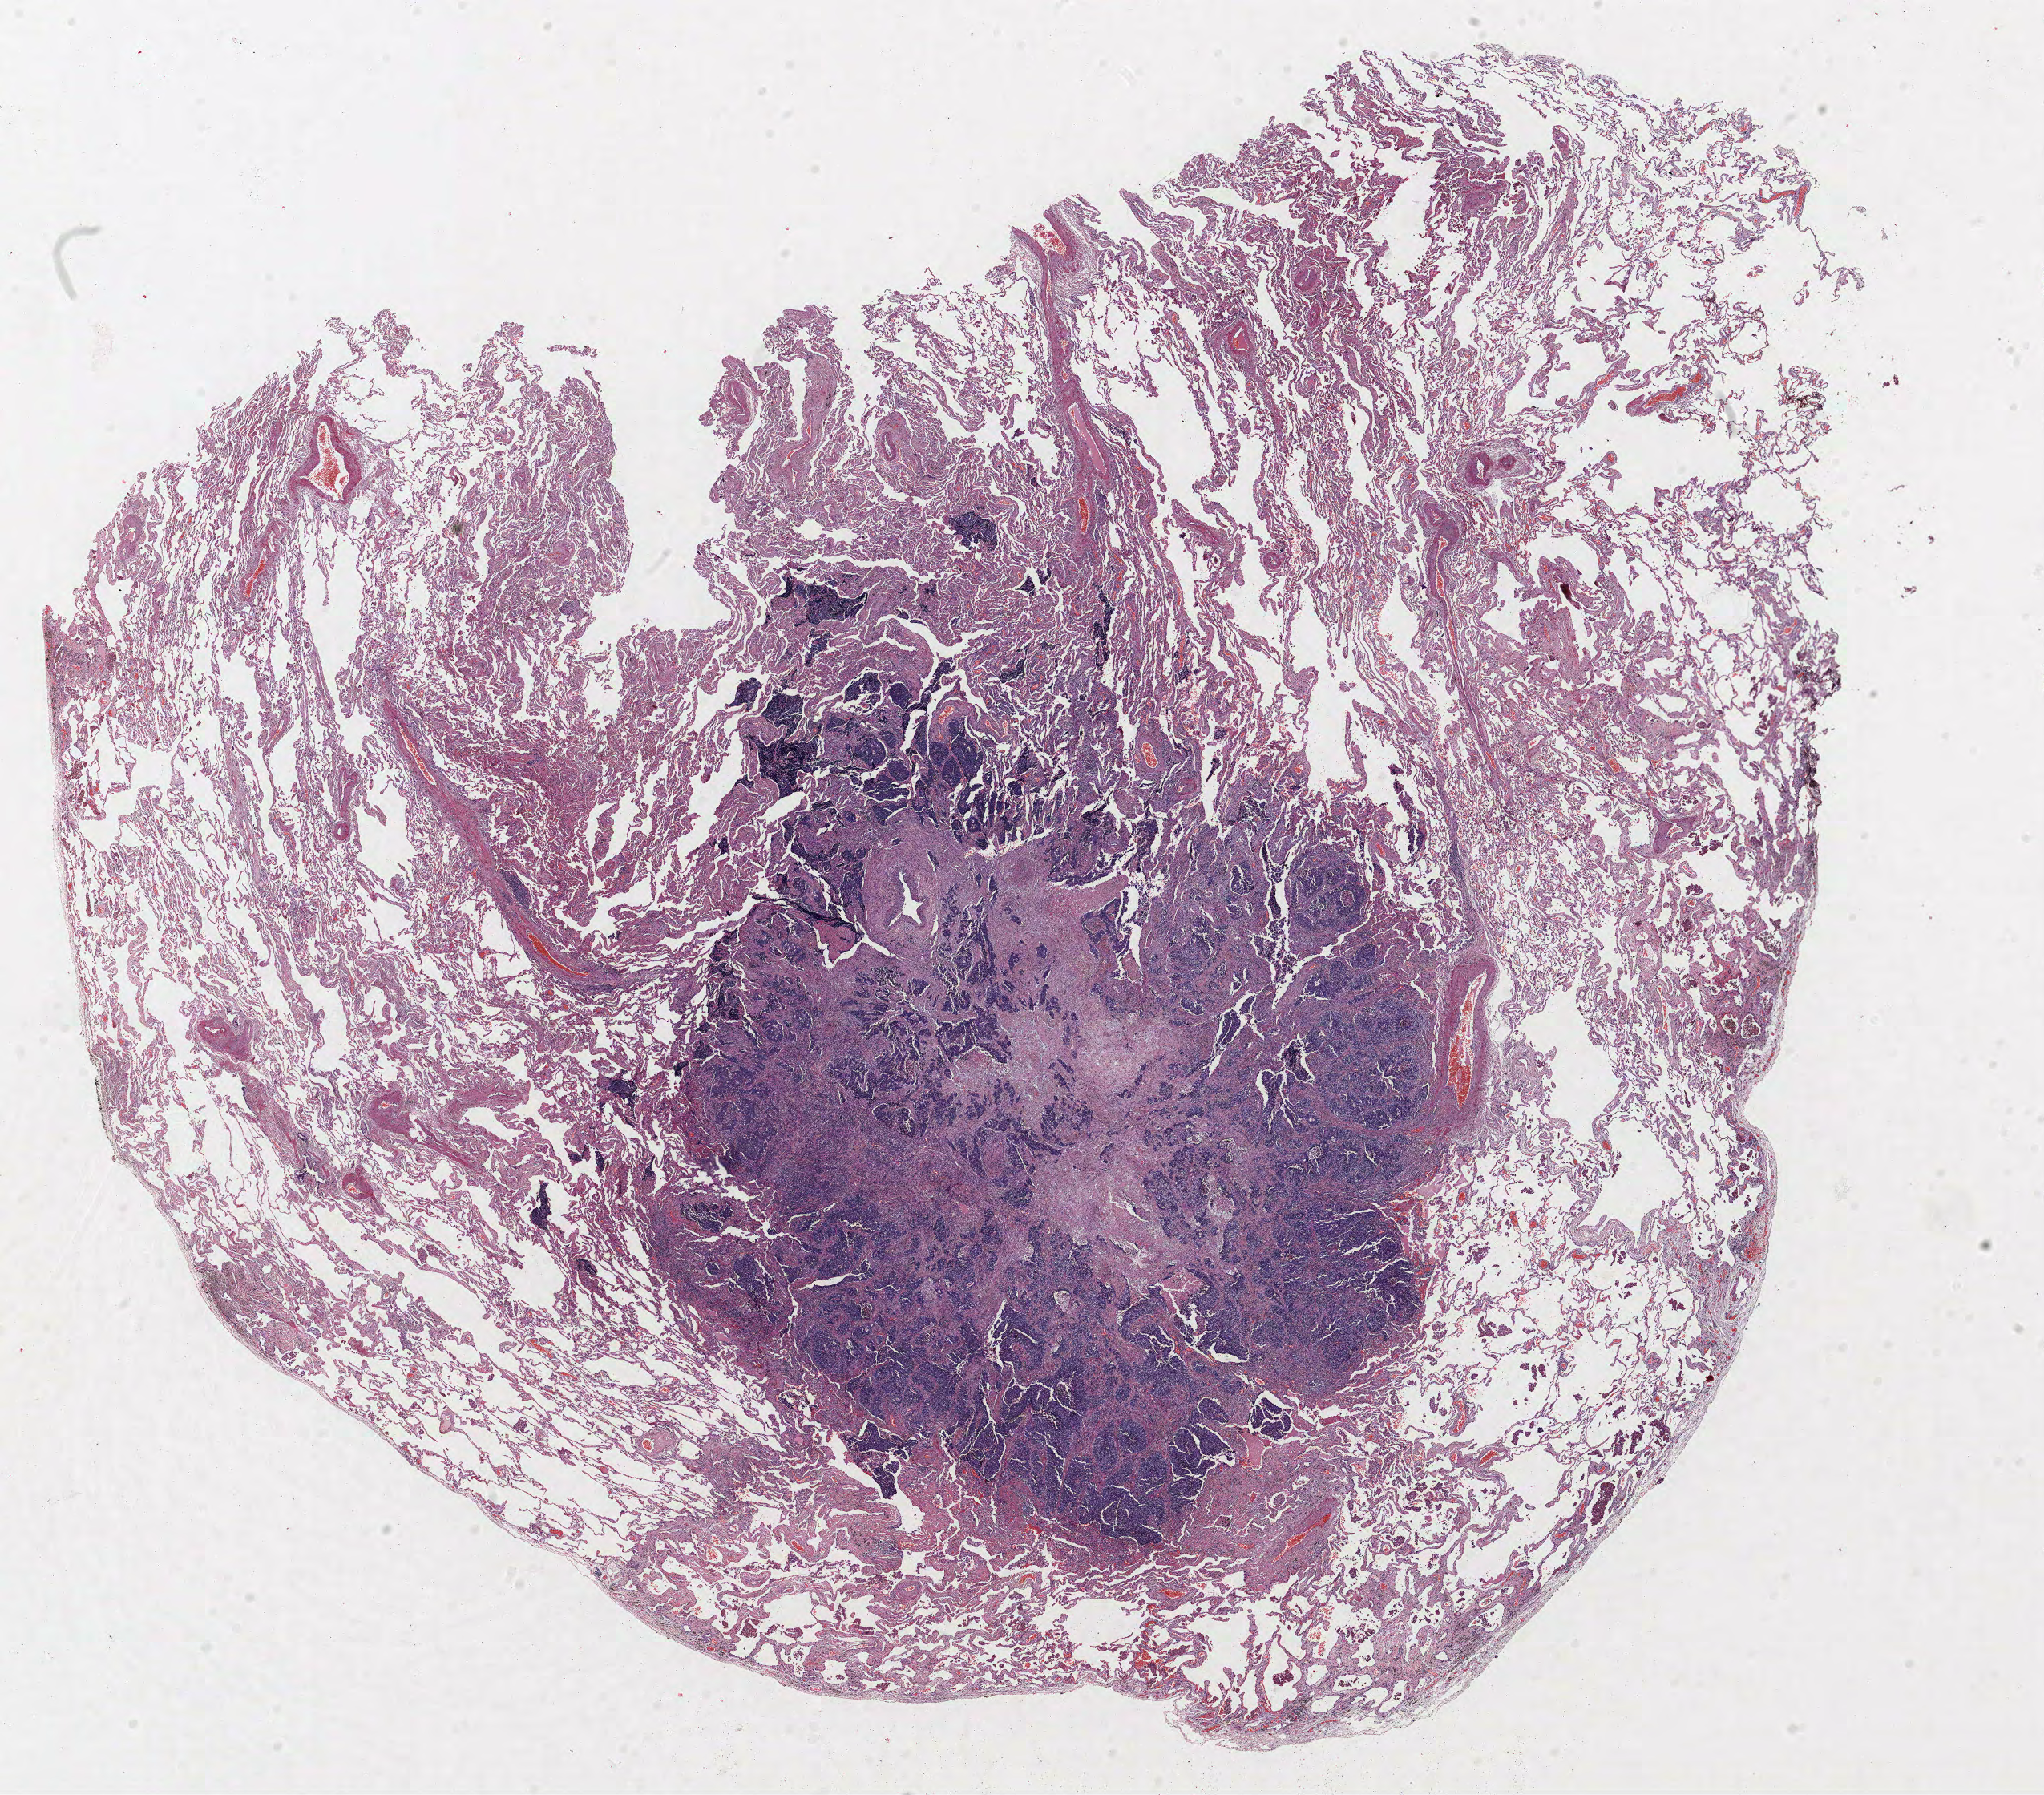
Hematoxylin and eosin (H&E) stained whole-slide image, low-resolution overview of the scanned area, about 20.4 x 17.9 mm (from a 40x scan). FFPE section. Lung. Male patient, aged 64 at enrolment. Current smoker at enrolment. Grade: poorly differentiated (G3).
Tumour size (pathology): 11 mm. Stage (AJCC 6th edition): IIIA. Participant's lung-cancer diagnosis: Neuroendocrine carcinoma, NOS. ICD-O-3 topography: upper lobe of lung (C34.1). Primary tumour location (clinical record): left upper lobe.